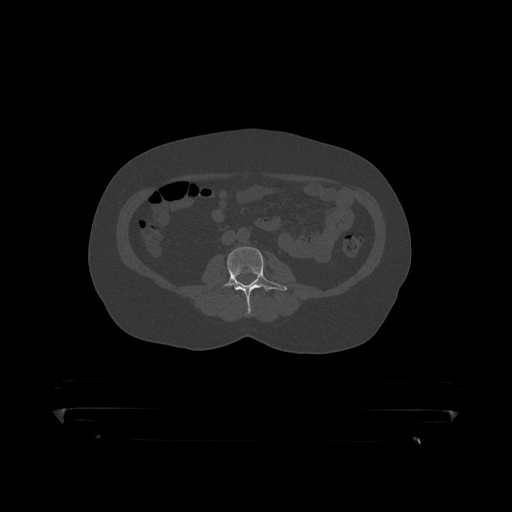
CT including the spine, one axial slice. Position 90 of 390 along the scan axis. 120 kVp. Bone window (W 1800 / L 400 HU). 512 × 512 image matrix, field of view 650 × 650 mm. Patient: male, 60 years. Case-level facts recorded for this patient, not image findings: primary cancer: prostate.
Structures marked on this image (semi-automatically segmented with operator editing):
- L2 vertebra: bounding box (x1, y1, x2, y2) in pixels: (248, 309, 251, 314)
- L3 vertebra: (219, 247, 287, 310)